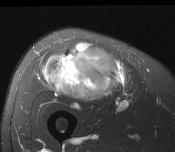
MRI of an extremity soft-tissue mass, one axial slice; position 79 of 116 along the scan axis; T2-weighted fat-saturated; MR volume resampled by the dataset authors to the PET/CT grid (not the native acquisition matrix); 3.27 mm slice thickness; 175 × 152 image matrix. Male patient. From the clinical record (not read from this slice): histological type: pleiomorphic leiomyosarcoma; grade: intermediate; site of the primary tumour: right thigh.
Annotated regions visible in this slice (expert contour drawn on MRI and transferred to this co-registered scan by the dataset authors):
- gross tumour volume including surrounding oedema: bounding box (x1, y1, x2, y2) in pixels: (44, 45, 119, 101)
- gross tumour volume (mass): (44, 45, 119, 101)